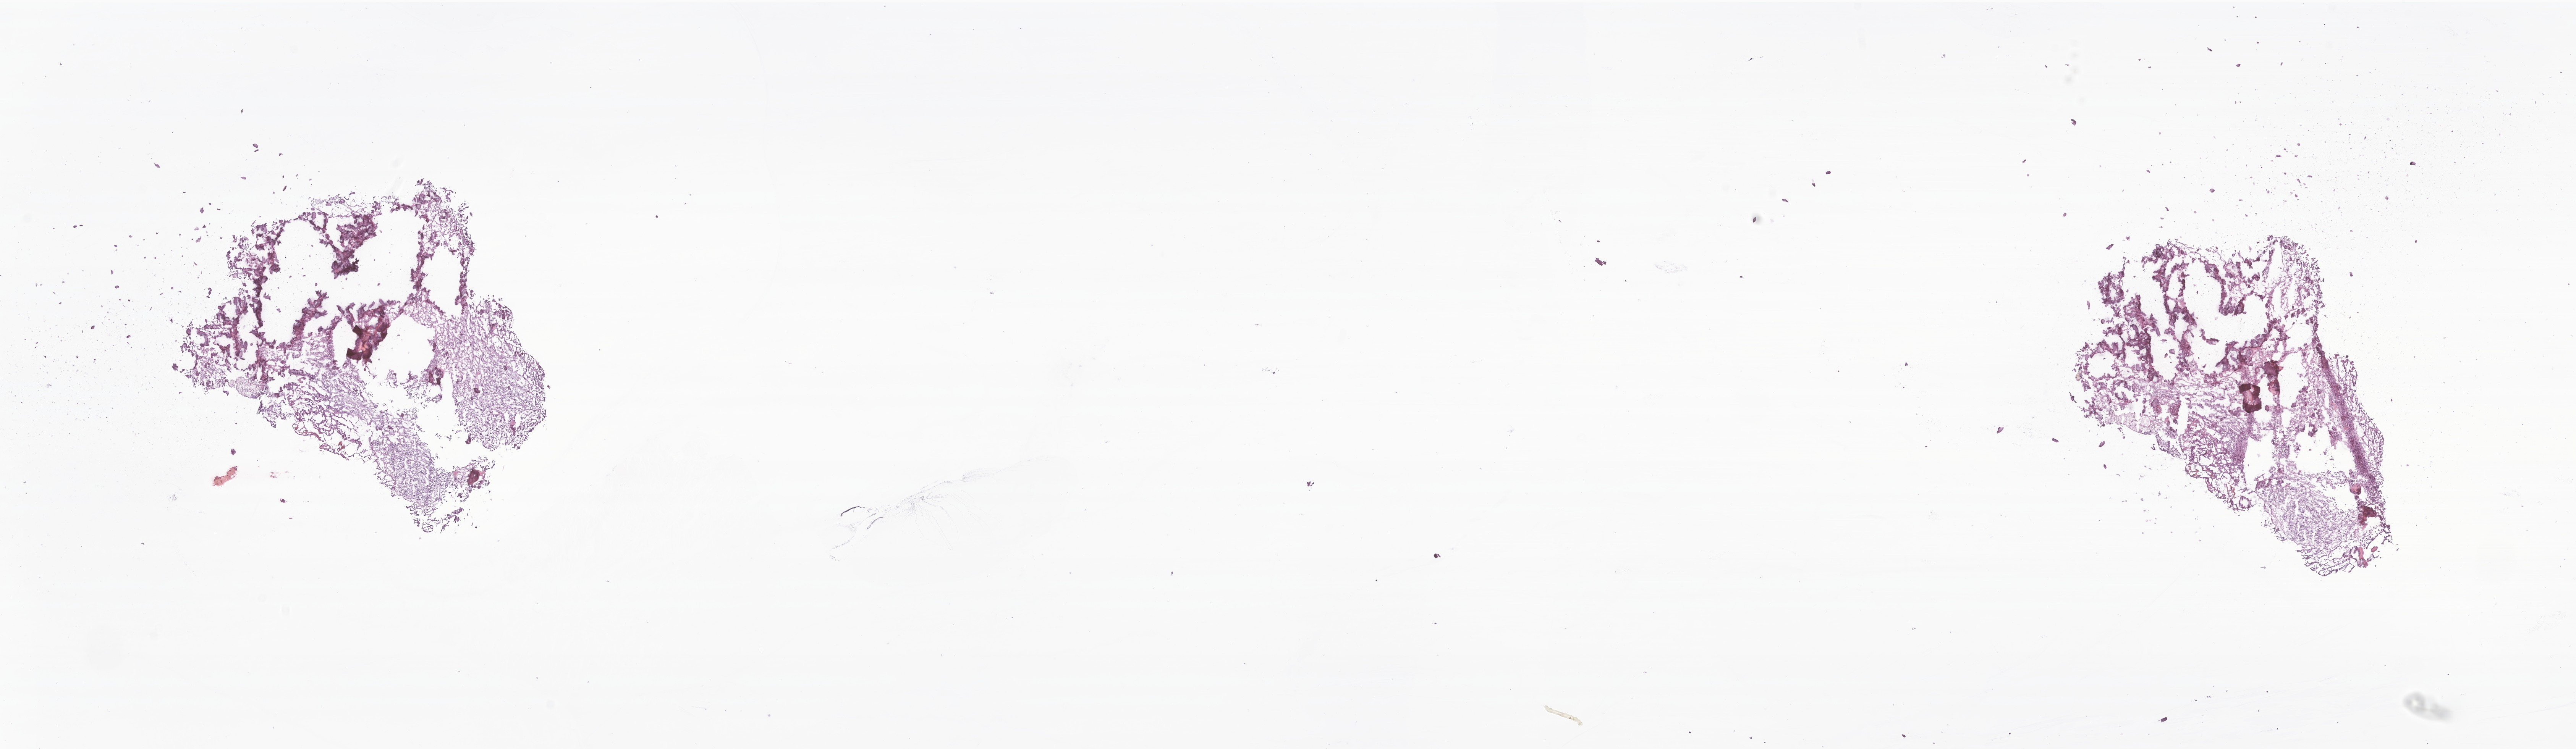
Digitized H&E-stained section of tumor tissue from the cerebral ventricle — whole scanned area (about 28.4 x 8.3 mm) shown as a low-resolution overview; frozen section. Patient male; age 133 months (11 years 1 month).
Diagnosis (ICD-O-3 morphology term): Choroid plexus papilloma, NOS.